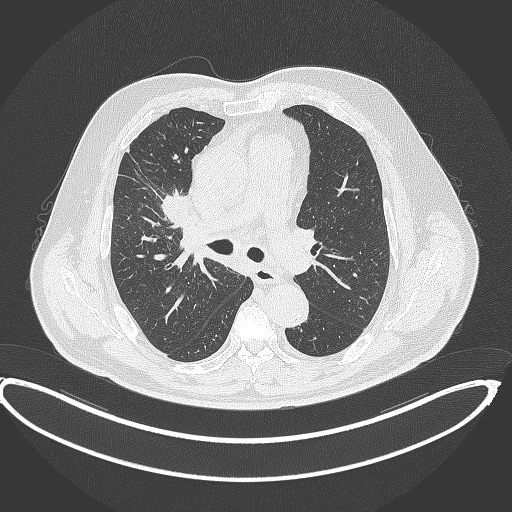
Chest CT, one axial slice; position 256 of 390 along the scan axis; lung window (W 1500 / L -600 HU); 512 × 512 image matrix, field of view 448 × 448 mm. Male patient, age 62 years. Case-level facts recorded for this patient, not image findings: clinical TNM (as recorded): T1c N3 M1c.
Structures marked on this image (bounding box drawn by a radiologist):
- lung tumour (recorded histology: adenocarcinoma): bounding box (x1, y1, x2, y2) in pixels: (161, 194, 192, 224)